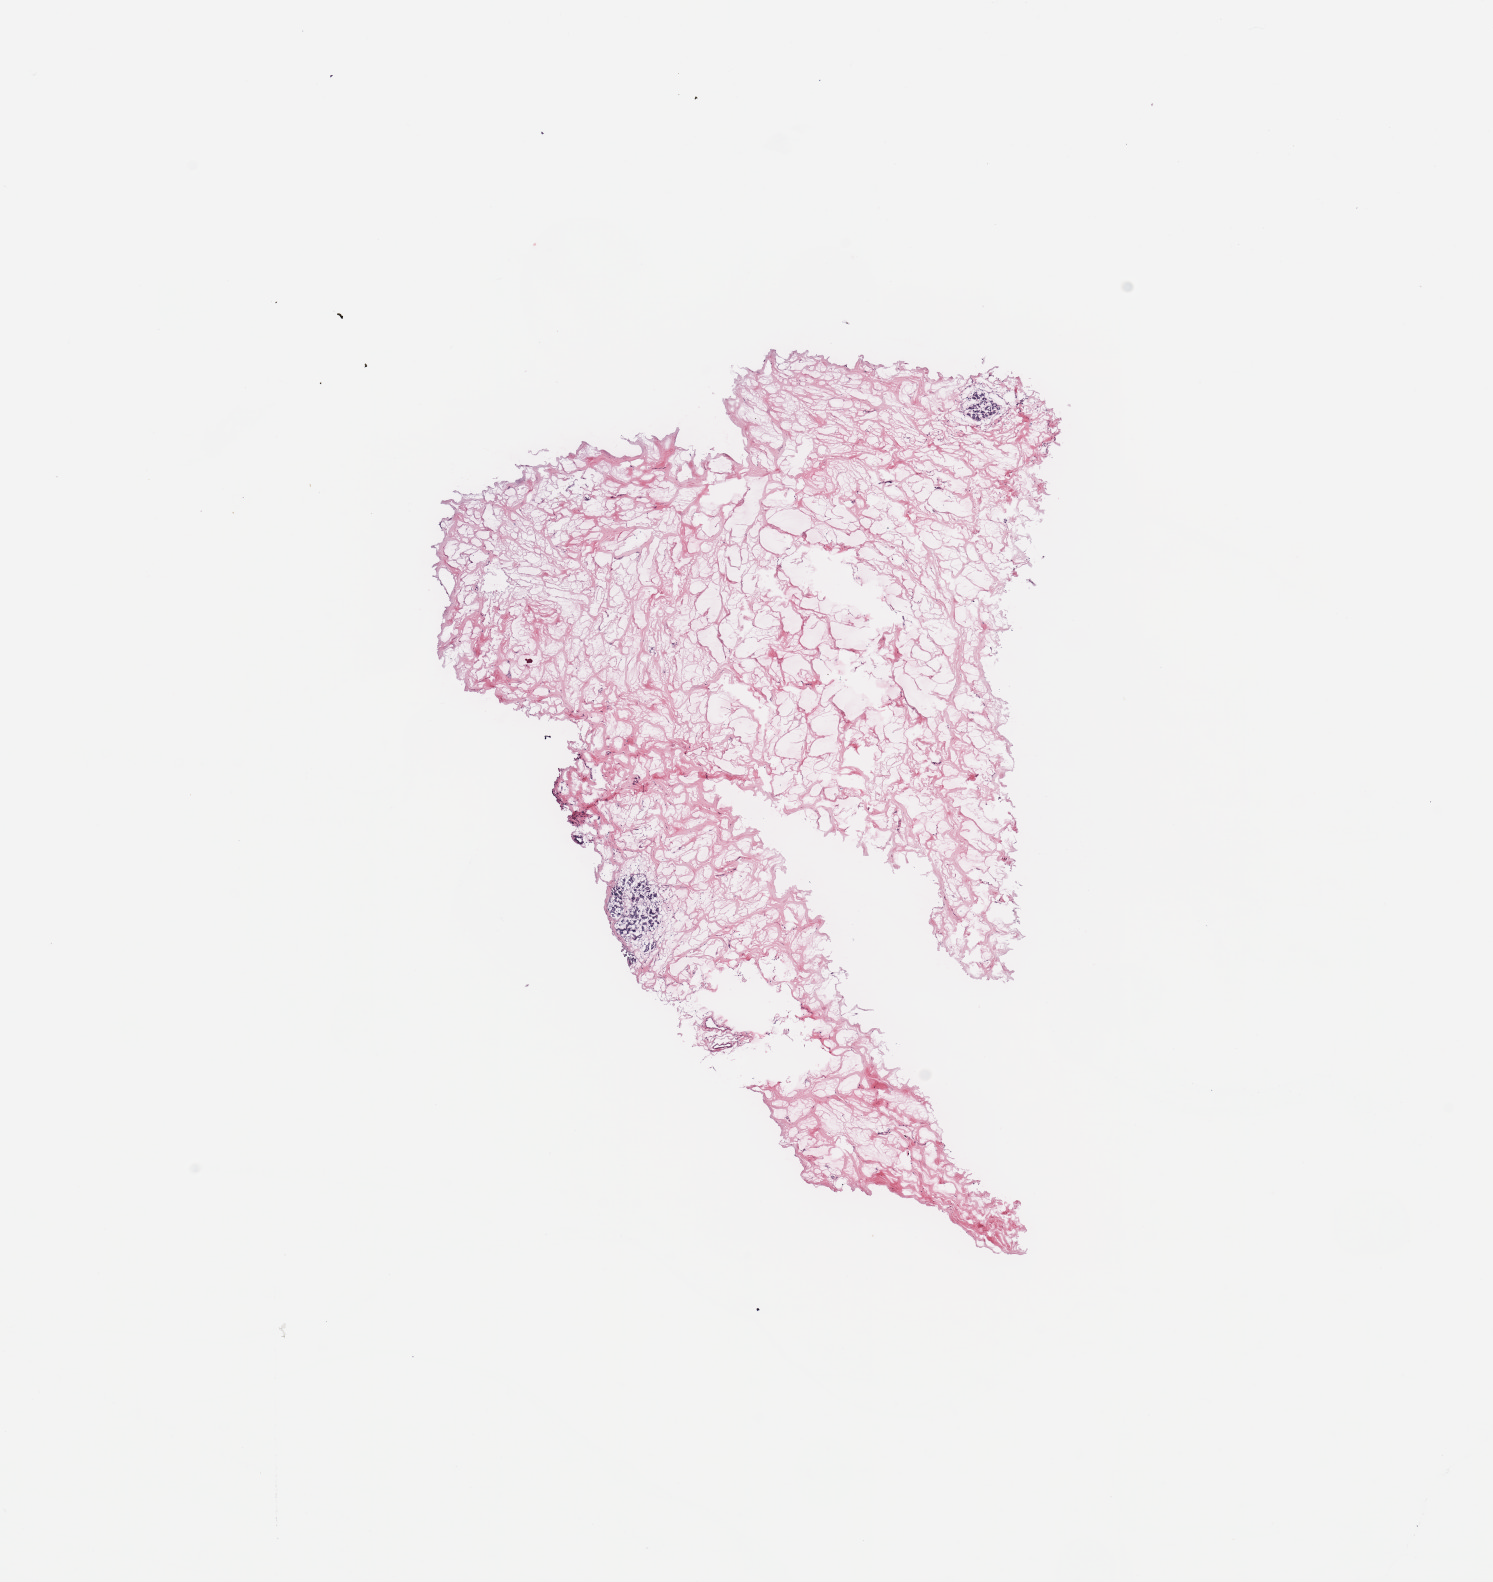
H&E-stained whole-slide image, shown as a low-resolution overview of the whole scanned area (about 11.8 x 12.5 mm, from a 20x scan); breast, tissue type not recorded.
Patient diagnosis (cohort enrolment): breast cancer (breast).